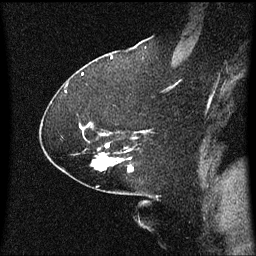
Breast MRI (dynamic contrast-enhanced), one sagittal slice; dynamic contrast-enhanced series, image 2 of 3 at this slice position (ordered by acquisition); 1.5 T; TE 4.2 ms, TR 8 ms; 256 × 256 image matrix, field of view 200 × 200 mm. Female patient, age 59 years.
Outlined on this slice (semi-automatically segmented with operator editing):
- analysis volume of interest (the breast-tissue region the enhancement analysis was run in; not a lesion): box from (x=86, y=140) to (x=135, y=173) px
- tumour enhancement mask (voxels above the 70 % enhancement threshold inside the analysis volume of interest): (x=92, y=150)–(x=133, y=171)